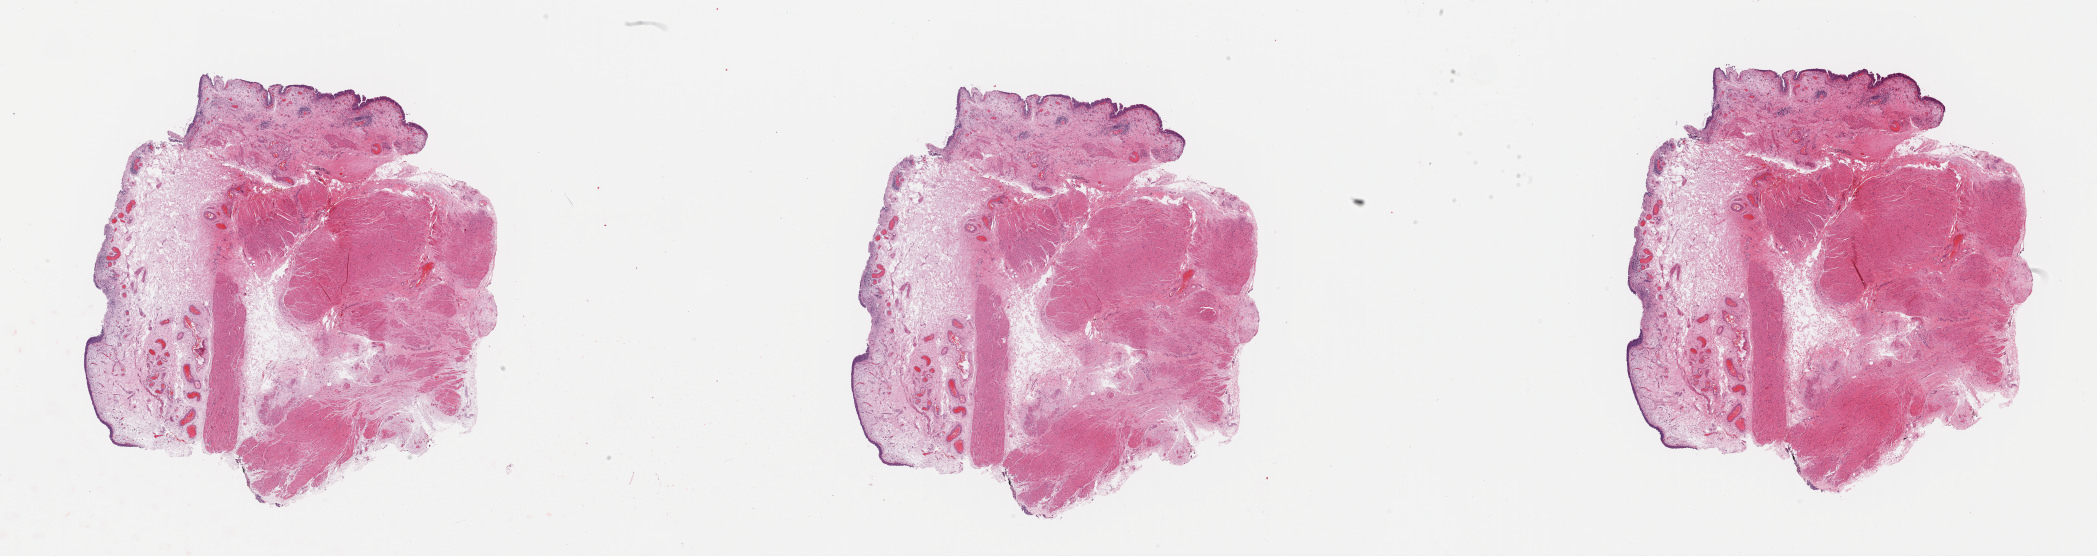
H&E whole-slide image, shown as a low-resolution overview of the whole scanned area (about 33.1 x 8.8 mm). Formalin-fixed paraffin-embedded (FFPE) diagnostic section. Sample: primary tumour, bladder. Female patient; age at initial diagnosis 53 years.
Histologic diagnosis: Transitional cell carcinoma.